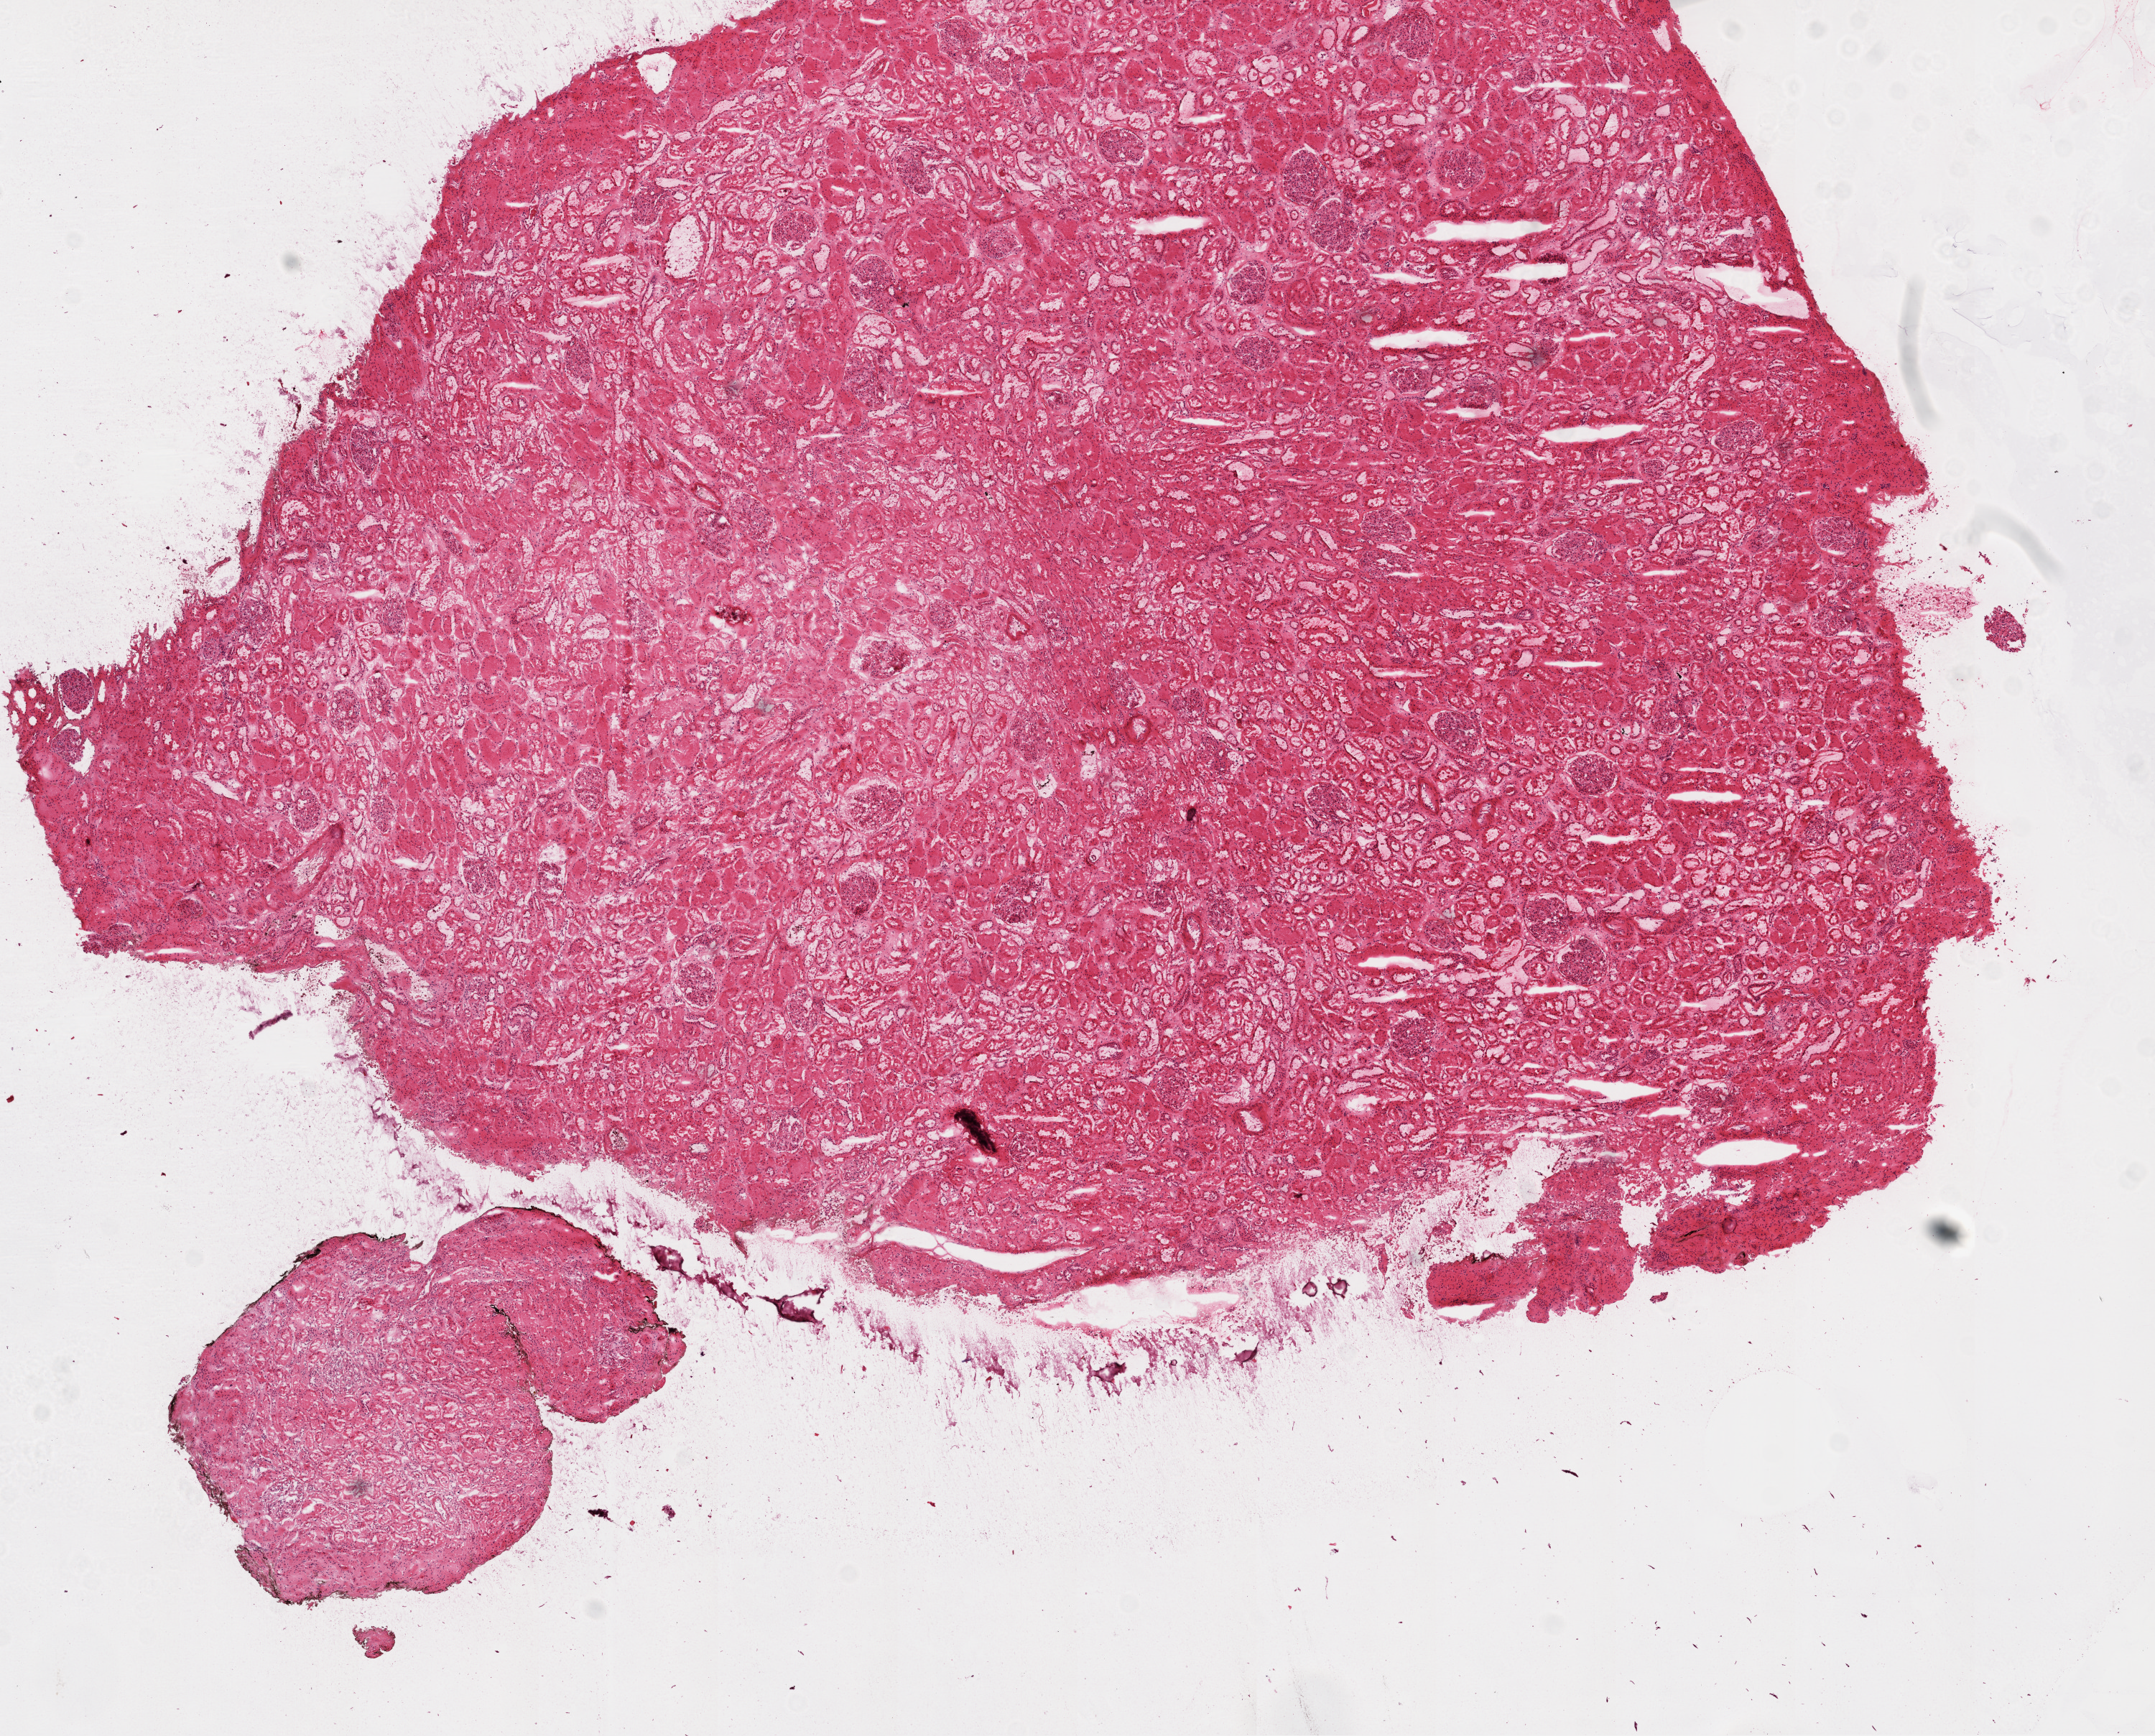
Digitized H&E-stained tissue section (whole slide), shown as a low-resolution overview of the whole scanned area (about 12.0 x 9.7 mm). Frozen section. Sample: solid tissue normal (non-tumour tissue), kidney. Male patient; age at initial diagnosis 53 years.
This section: solid tissue normal (non-tumour) sample from the same patient. Patient diagnosis: Clear cell adenocarcinoma, NOS.